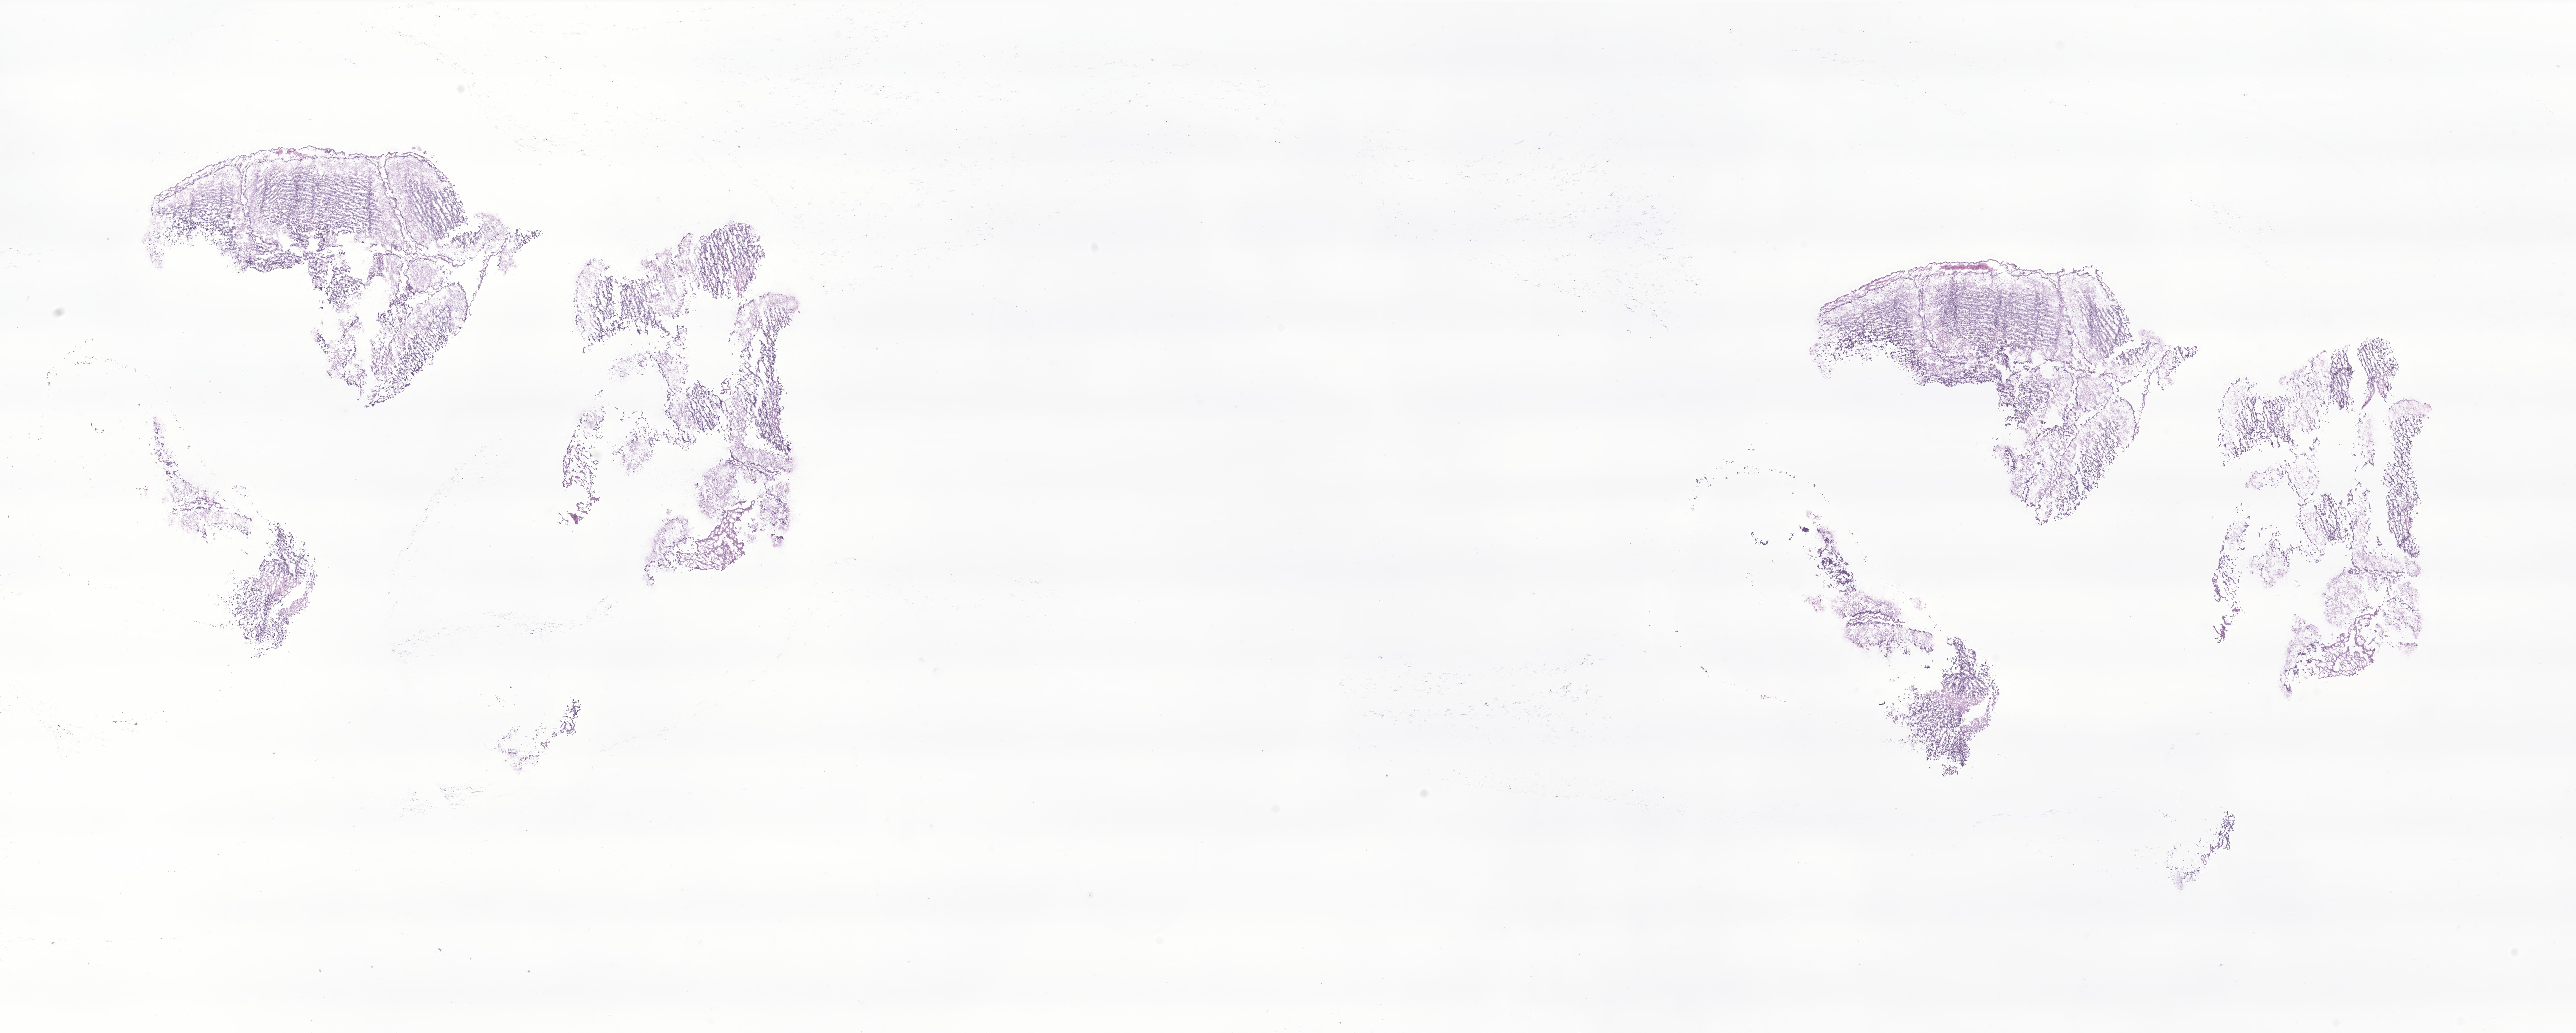
Haematoxylin and eosin whole-slide image of tumor tissue from the brain, whole scanned area (about 32.5 x 13.1 mm) shown as a low-resolution overview. Cryosection (OCT / tissue freezing medium). Patient: male, age 93 days.
Diagnosis: Atypical teratoid/rhabdoid tumor.